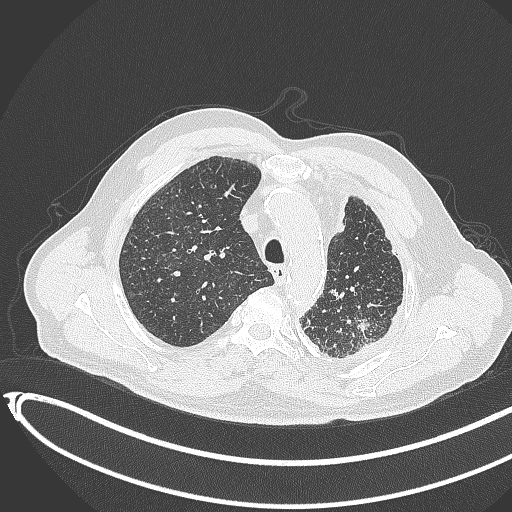
Chest CT, one axial slice. Position 333 of 451 along the scan axis. Lung window (W 1500 / L -600 HU). 1 mm slice thickness. 512 × 512 image matrix, field of view 400 × 400 mm. Patient: male, 78 years. From the clinical record (not read from this slice): clinical TNM (as recorded): T1c N0 M1.
Structures marked on this image (rectangle marked by the reading radiologist):
- lung tumour (recorded histology: adenocarcinoma): bounding box (x1, y1, x2, y2) in pixels: (353, 316, 375, 342)